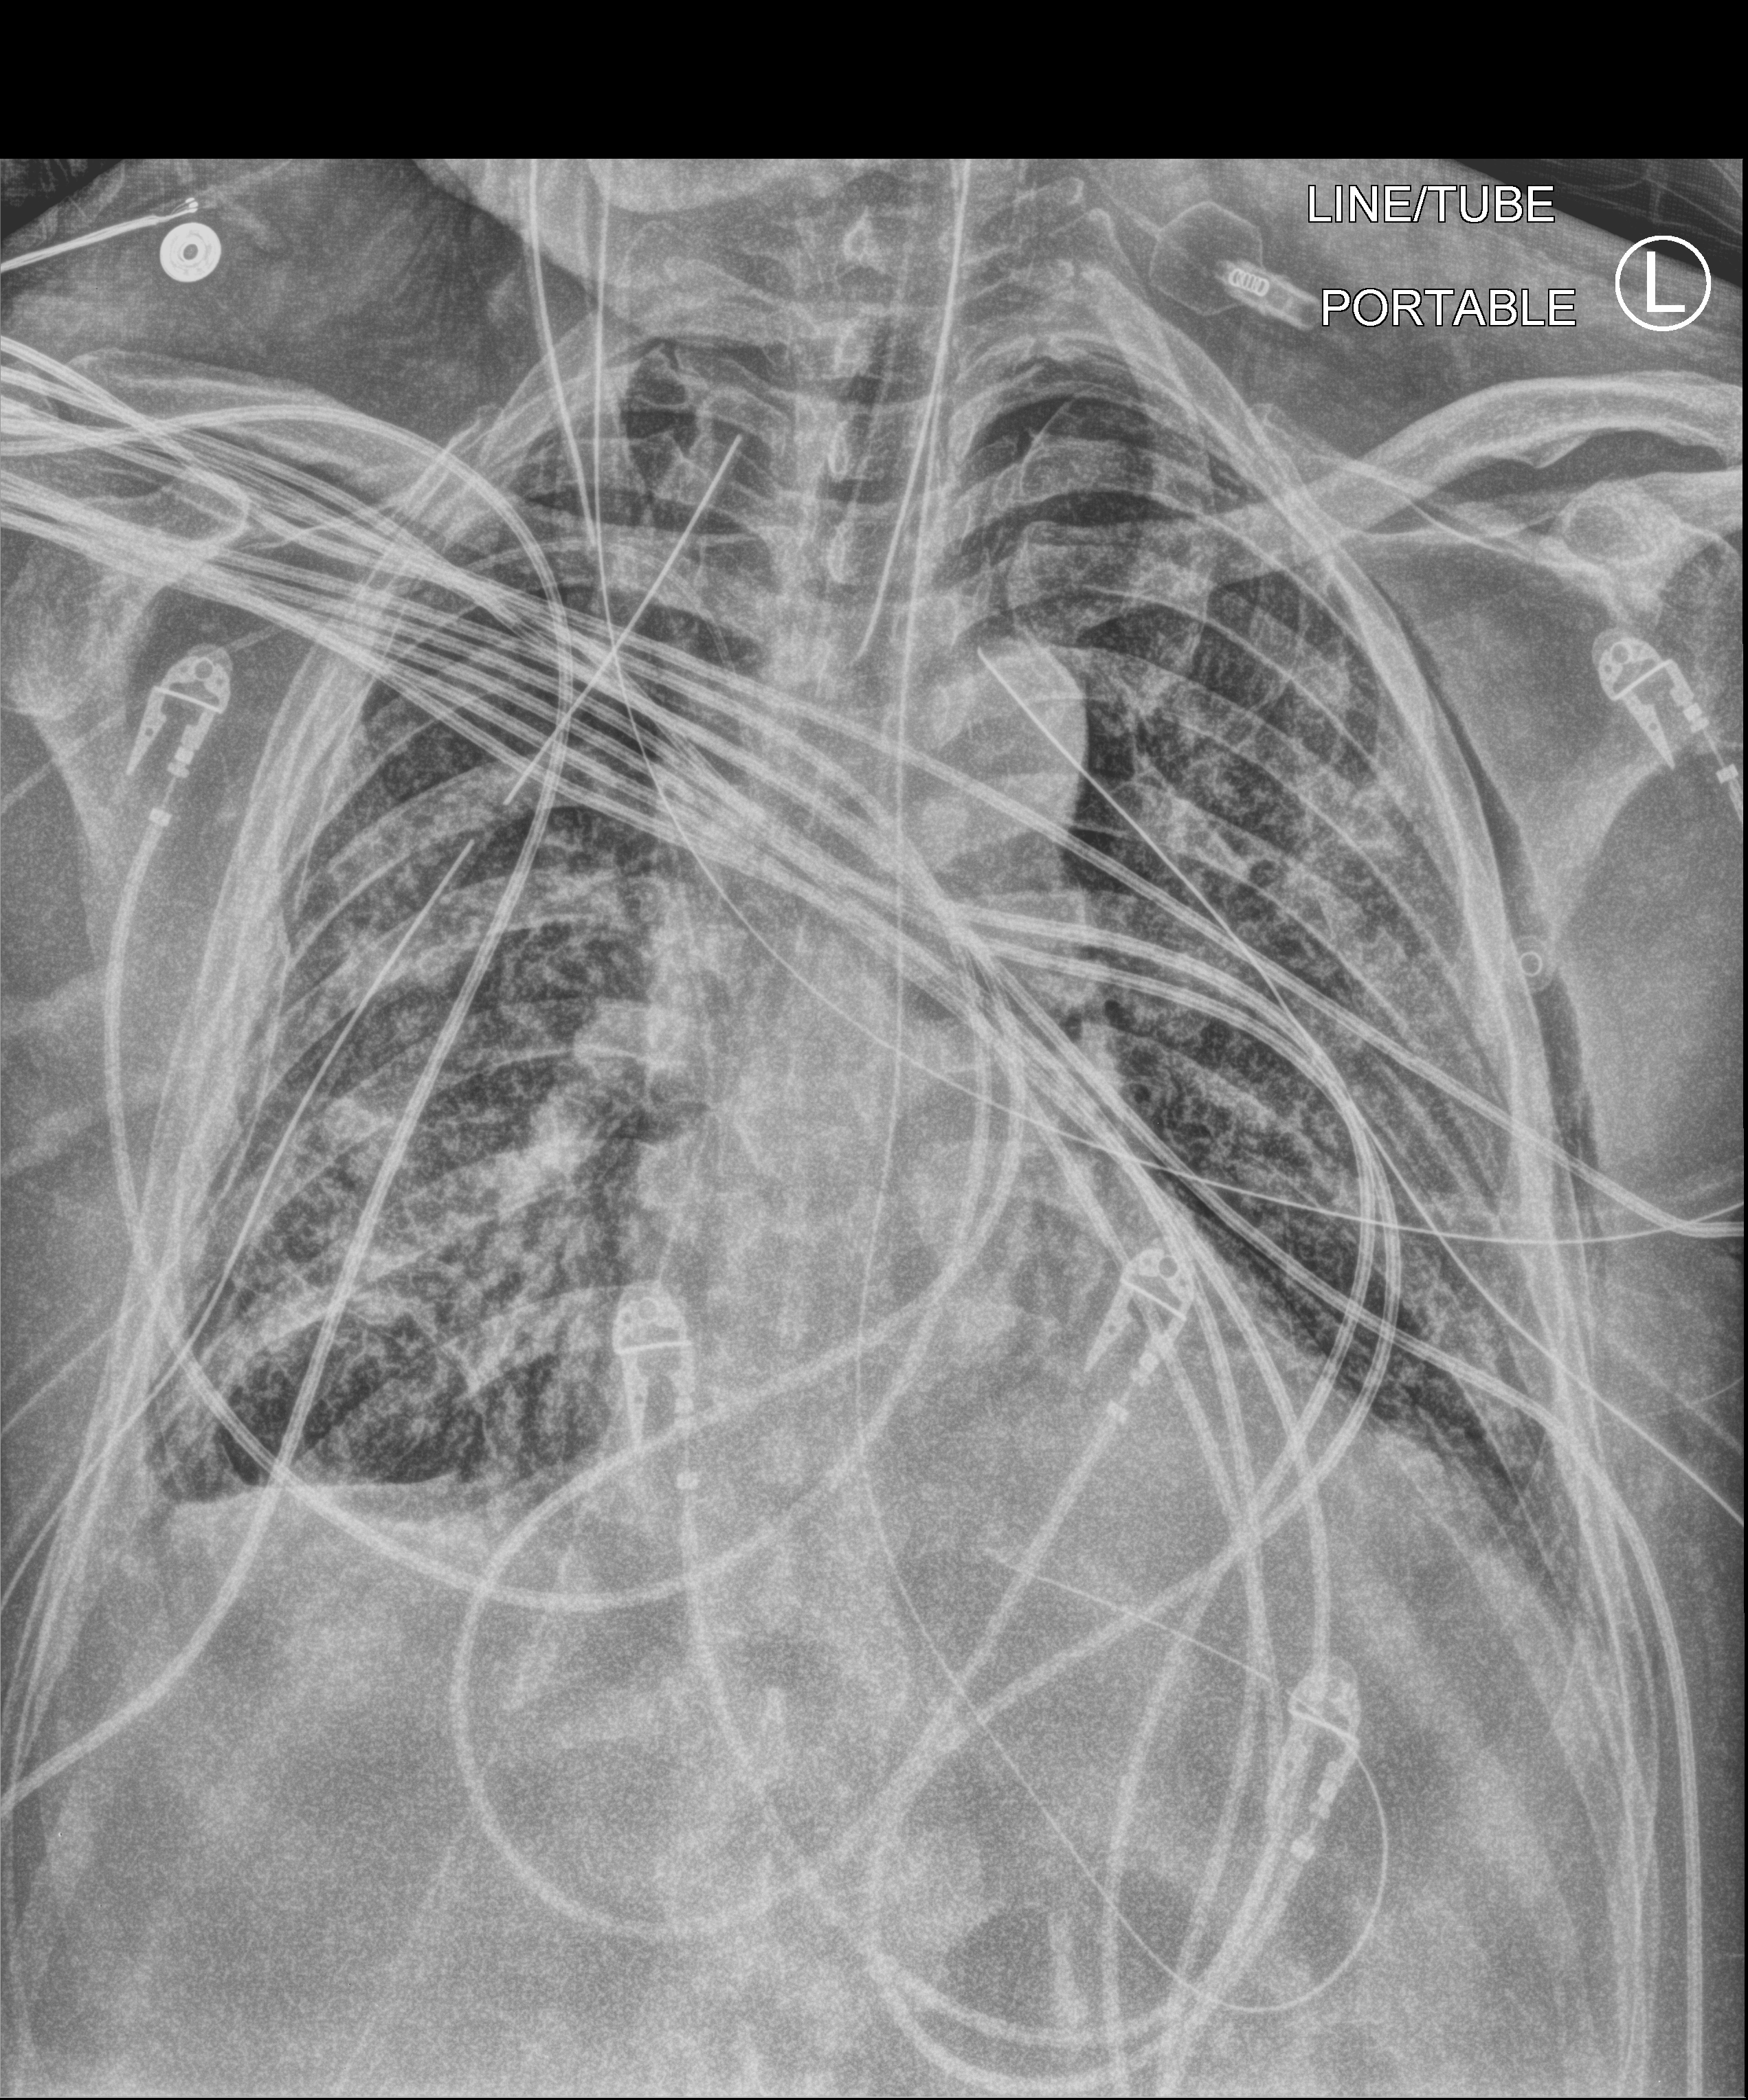
Portable chest radiograph; anteroposterior (AP) projection. Patient hospitalised with COVID-19; male, aged 60–74 years.
Hospital-stay facts (about this admission, not read from this image; timing relative to this image not recorded): mechanically ventilated during this hospital stay: yes.